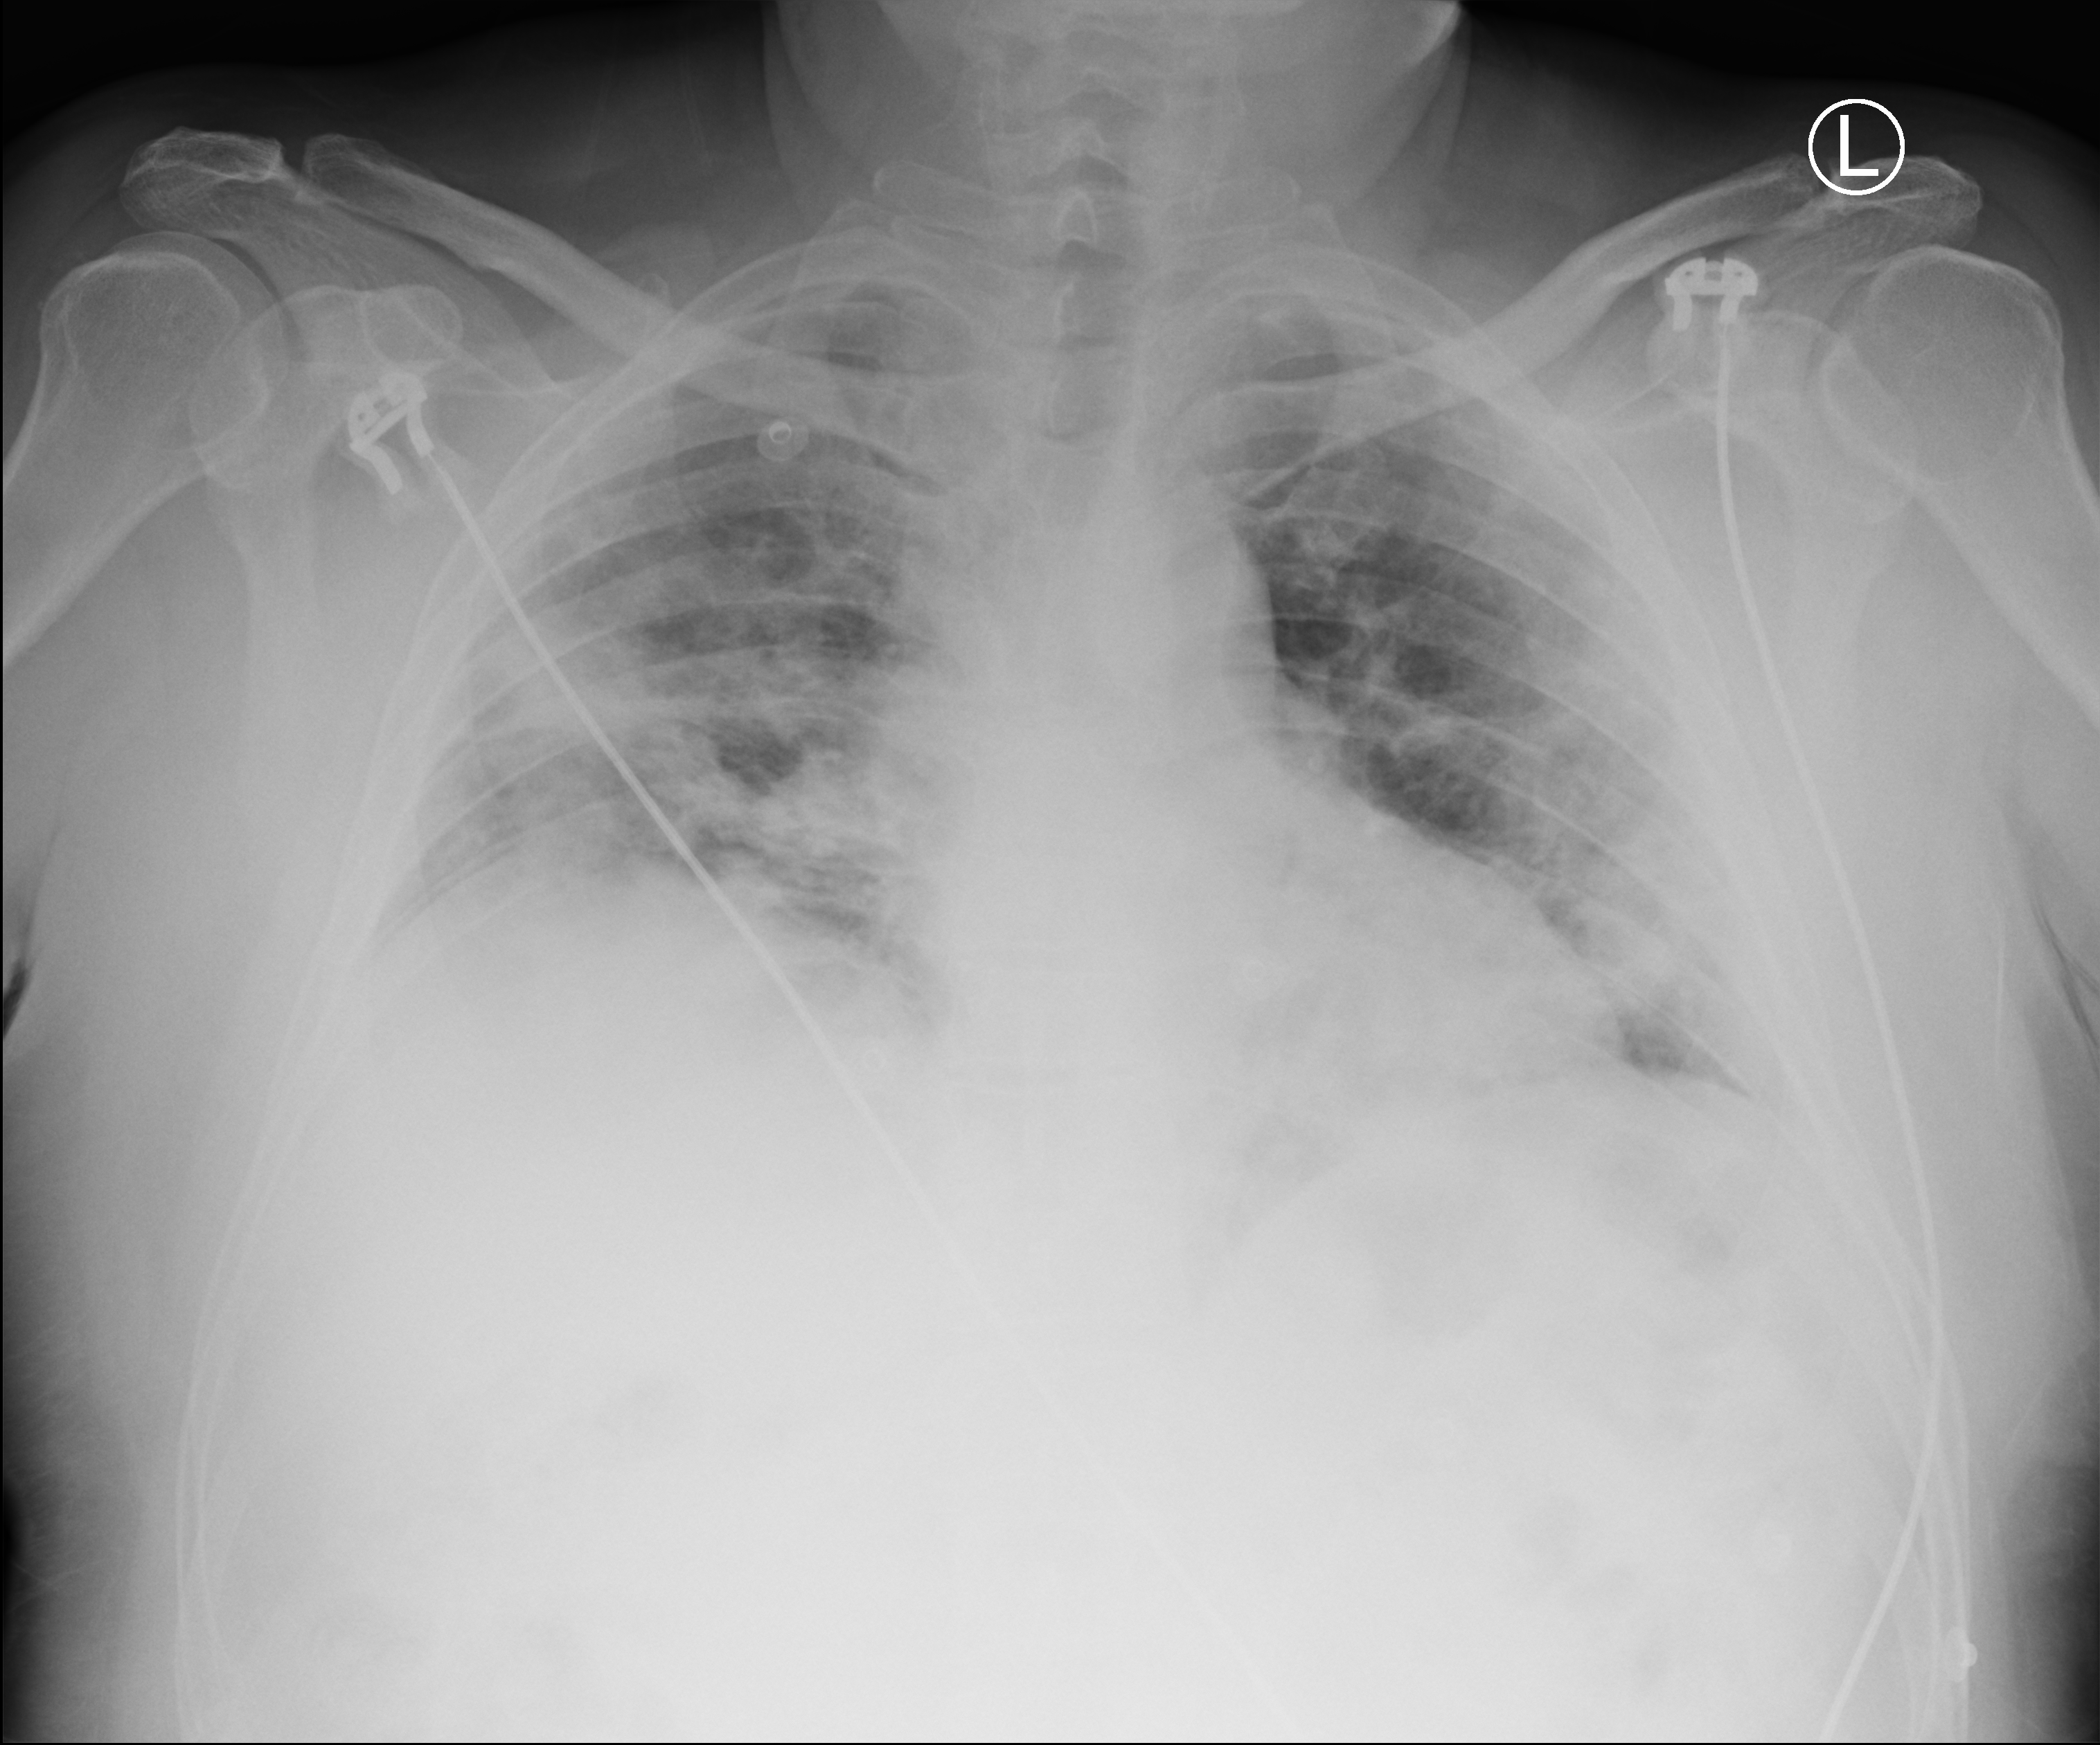
Chest radiograph. Patient hospitalised with COVID-19; male, aged 60–74 years.
Hospital-stay facts (about this admission, not read from this image; timing relative to this image not recorded):
- admitted to intensive care during this hospital stay: no